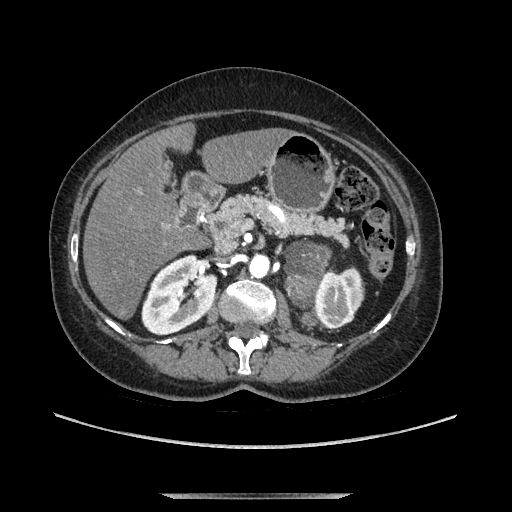
Contrast-enhanced abdominal CT, one axial slice. Slice 60 of 169 in the series (ordered by position). Soft-tissue window (W 400 / L 40 HU). 1.25 mm slice thickness. 512 × 512 image matrix. Female patient. From the clinical record (not read from this slice): diagnosis: adrenocortical carcinoma; tumour side: left adrenal; tumour size at pathology: 9 cm; Ki-67 index: 2 %; stage (as recorded): 3.
Annotated regions visible in this slice (semi-automatic segmentation, software-assisted and operator-edited):
- mass: bounding box (x1, y1, x2, y2) in pixels: (286, 245, 329, 307)